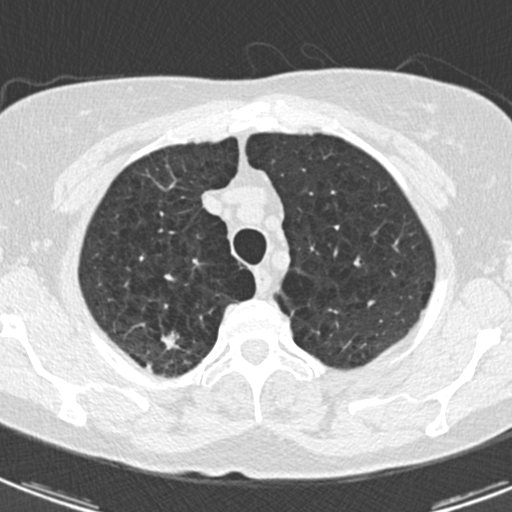
Low-dose screening chest CT, one axial slice. Position 148 of 174 along the scan axis. Reconstruction kernel B30f. 120 kVp. Lung window (W 1500 / L -600 HU). 512 × 512 image matrix, field of view 281 × 281 mm.
Annotated regions visible in this slice (outlined manually by an expert reader):
- lesion 1 (tumor, upper lobe of right lung): bounding box [x1, y1, x2, y2] px = [160, 331, 179, 350]